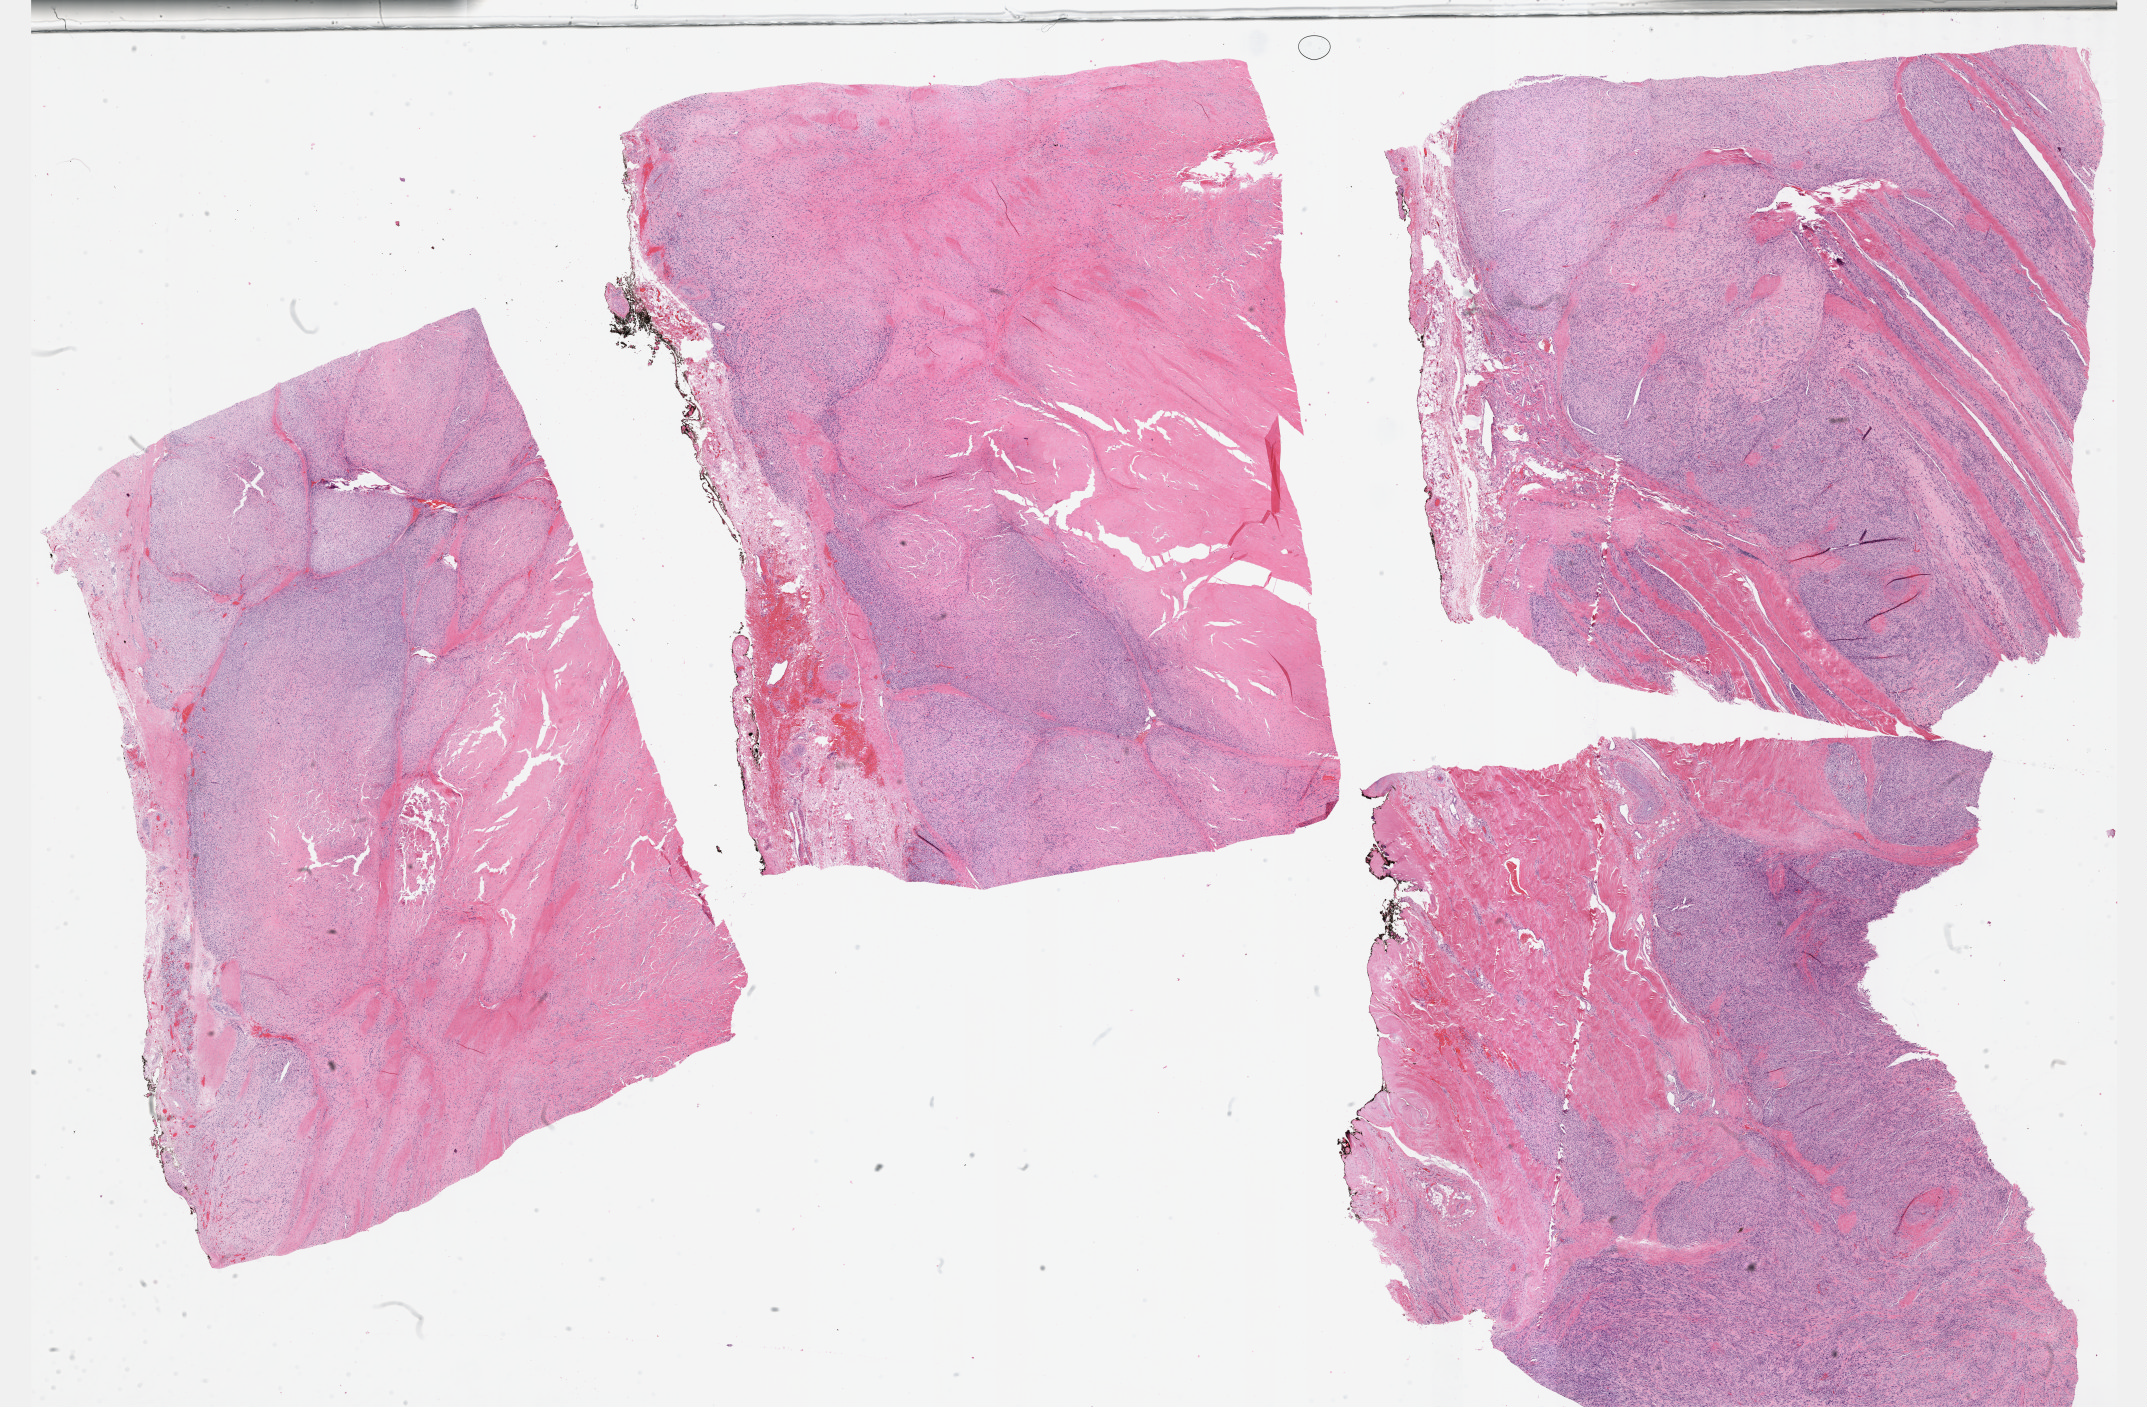
Digitized H&E tissue section (whole slide) — a low-resolution overview of the entire scanned area, about 34.7 x 22.7 mm. Formalin-fixed paraffin-embedded (FFPE) diagnostic section. Sample: primary tumour, connective, subcutaneous and other soft tissues. Male patient; age at initial diagnosis 74 years.
Diagnosis: Leiomyosarcoma, NOS (connective, subcutaneous and other soft tissues of lower limb and hip).